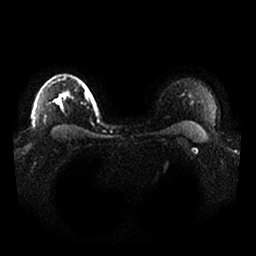
Breast MRI, one axial slice; position 24 of 25 along the scan axis; diffusion-weighted series; image 2 of 4 stored at this slice position (different b-values; order by instance number); 1.5 T; 4 mm slice thickness; 256 × 256 image matrix. Female patient.
Outlined on this slice (outlined manually by an expert reader):
- tumour on diffusion-weighted imaging: bounding box <57,100,60,103> (left, top, right, bottom; pixels)